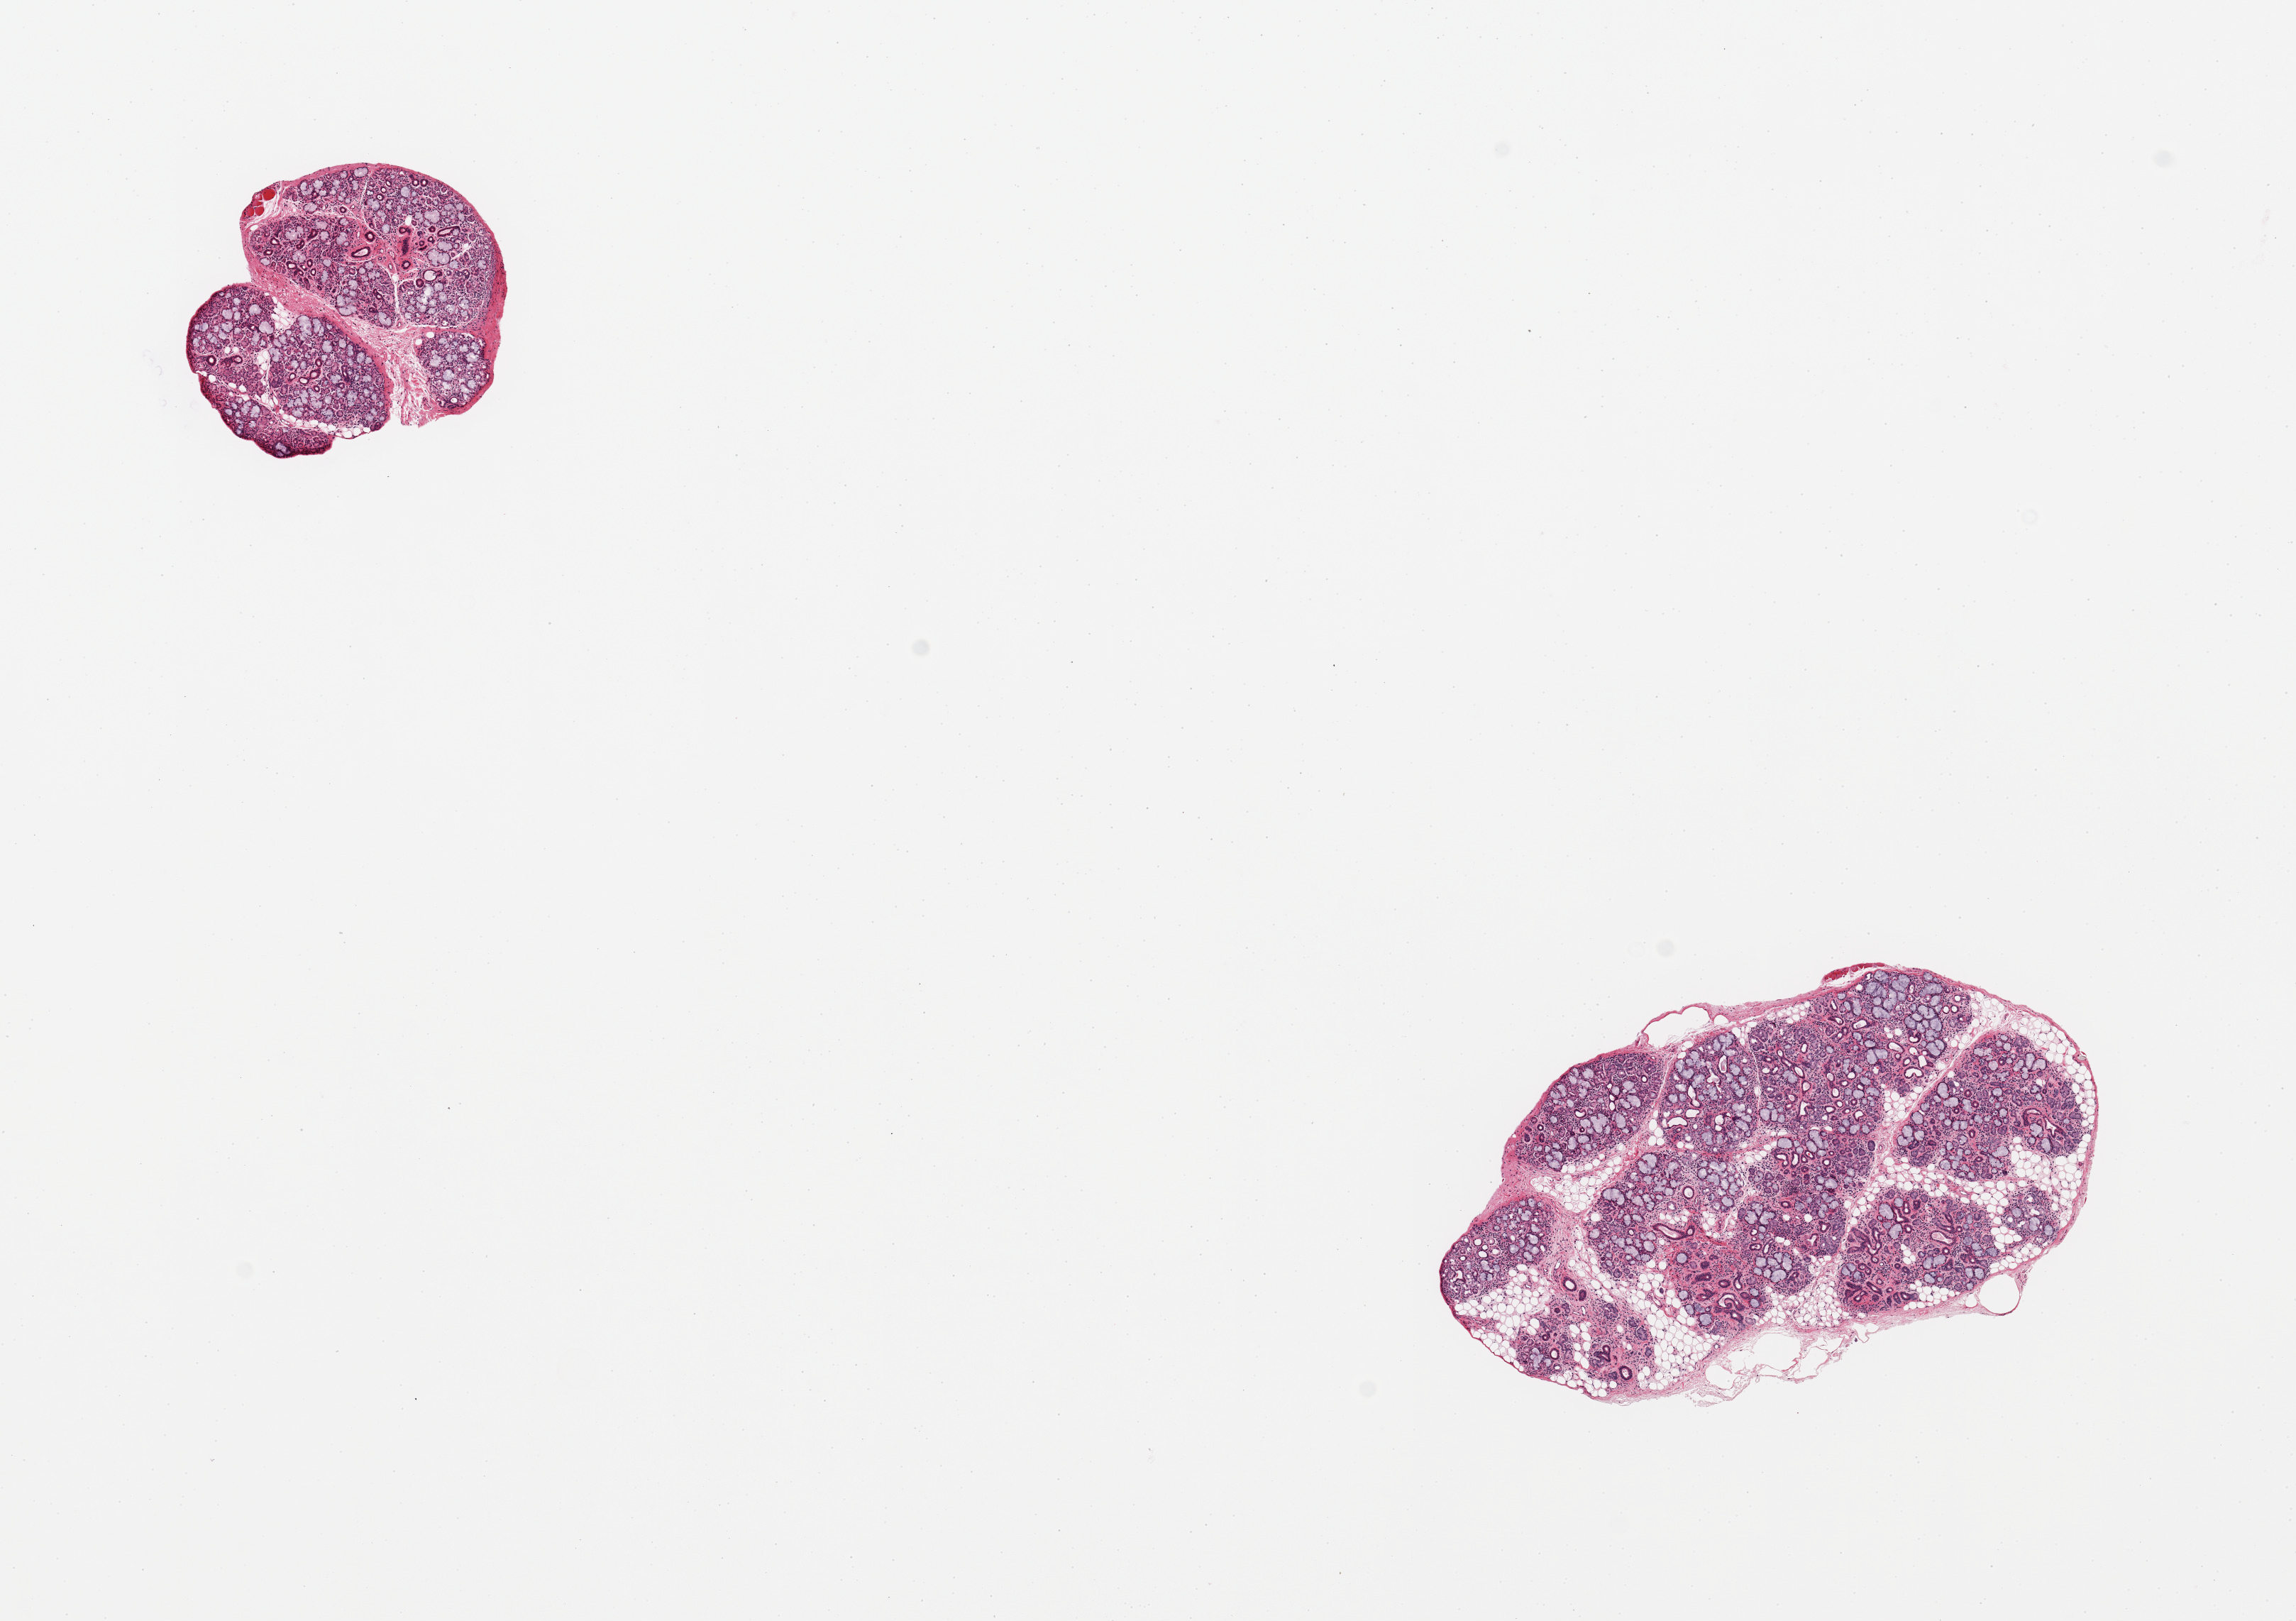
Whole-slide image, hematoxylin and eosin (H&E) stain, shown as a low-resolution overview of the whole scanned area (about 12.8 x 9.0 mm, from a 20x scan); PAXgene-fixed, paraffin-embedded tissue; section of minor salivary gland (target tissue); donor tissue sample. Male donor.
* pathologist's review note for this sample: 2 pieces; well dissected; mild to moderate diffuse lymphocytic infiltrate; 1 piece has 20% internal fat content